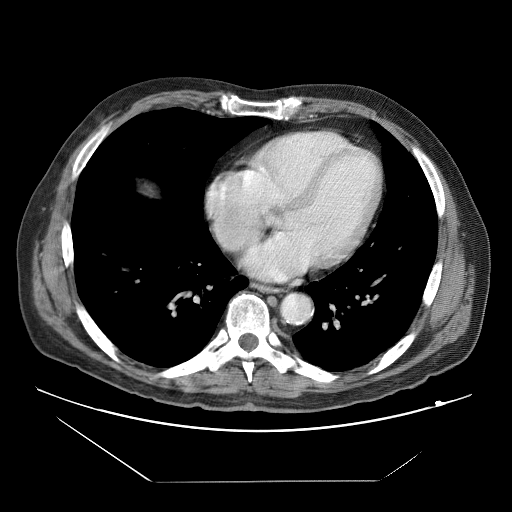
Contrast-enhanced abdominal CT (liver protocol), one axial slice; slice 78 of 83 in the series (ordered by position); reconstruction kernel STANDARD; soft-tissue window (W 400 / L 40 HU); 512 × 512 image matrix, field of view 420 × 420 mm. Case-level facts recorded for this patient, not image findings: diagnosis: hepatocellular carcinoma (patient treated with transarterial chemoembolisation; whether this scan precedes or follows treatment is not stated here); TNM stage (as recorded): Stage-IVB; Child-Pugh class: B; tumour differentiation: poorly differentiated; tumour nodularity: uninodular.
Outlined on this slice (semi-automatically segmented with operator editing):
- liver parenchyma outside the tumour (the mass and vessels are separate outlines, so this box may not span the whole liver): bounding box <142,184,154,194> (left, top, right, bottom; pixels)